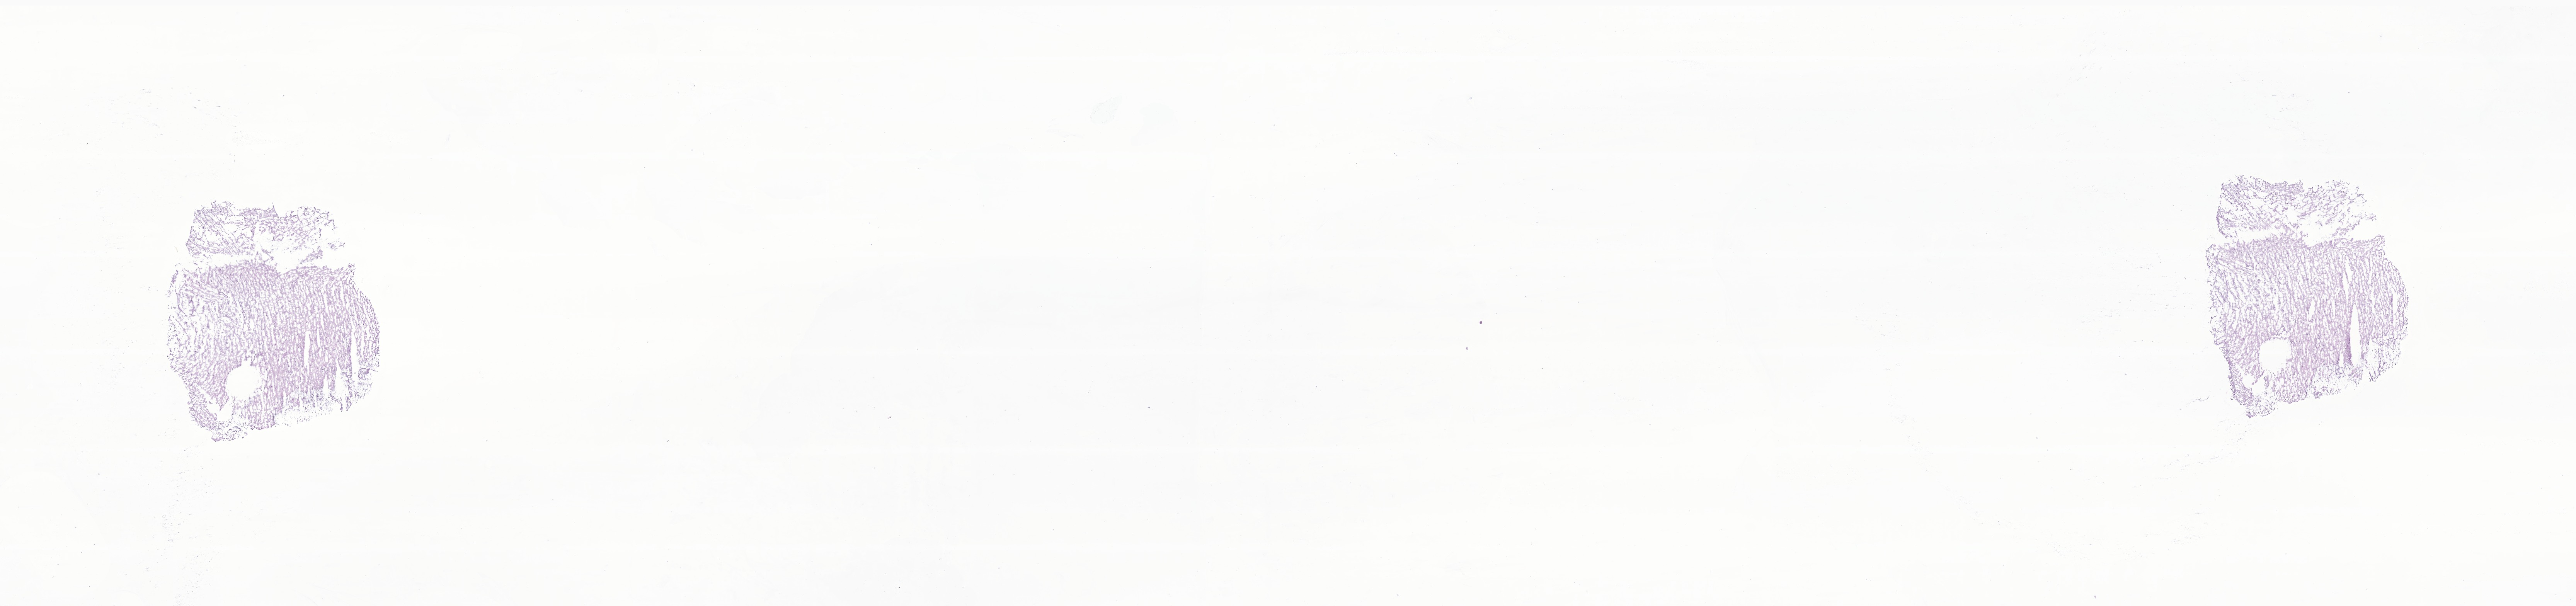
Digitized haematoxylin and eosin-stained section of tumor tissue from the brain — whole scanned area (about 28.1 x 6.6 mm) shown as a low-resolution overview, frozen section. Patient male; age 136 months (11 years 4 months).
• diagnosis (ICD-O-3 morphology term): Dysembryoplastic neuroepithelial tumor